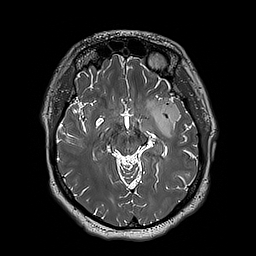
Brain MRI from a brain-tumour surgery series, one axial slice; slice 113 of 192 in the series (ordered by position); 1 mm slice thickness; 256 × 256 image matrix, field of view 250 × 250 mm. From the clinical record (not read from this slice): histopathology: Astrocytoma; WHO grade: 3; IDH mutation: yes; tumour location: Left Insular.
Annotated regions visible in this slice (manually delineated by an expert):
- tumour: box from (x=148, y=98) to (x=181, y=138) px